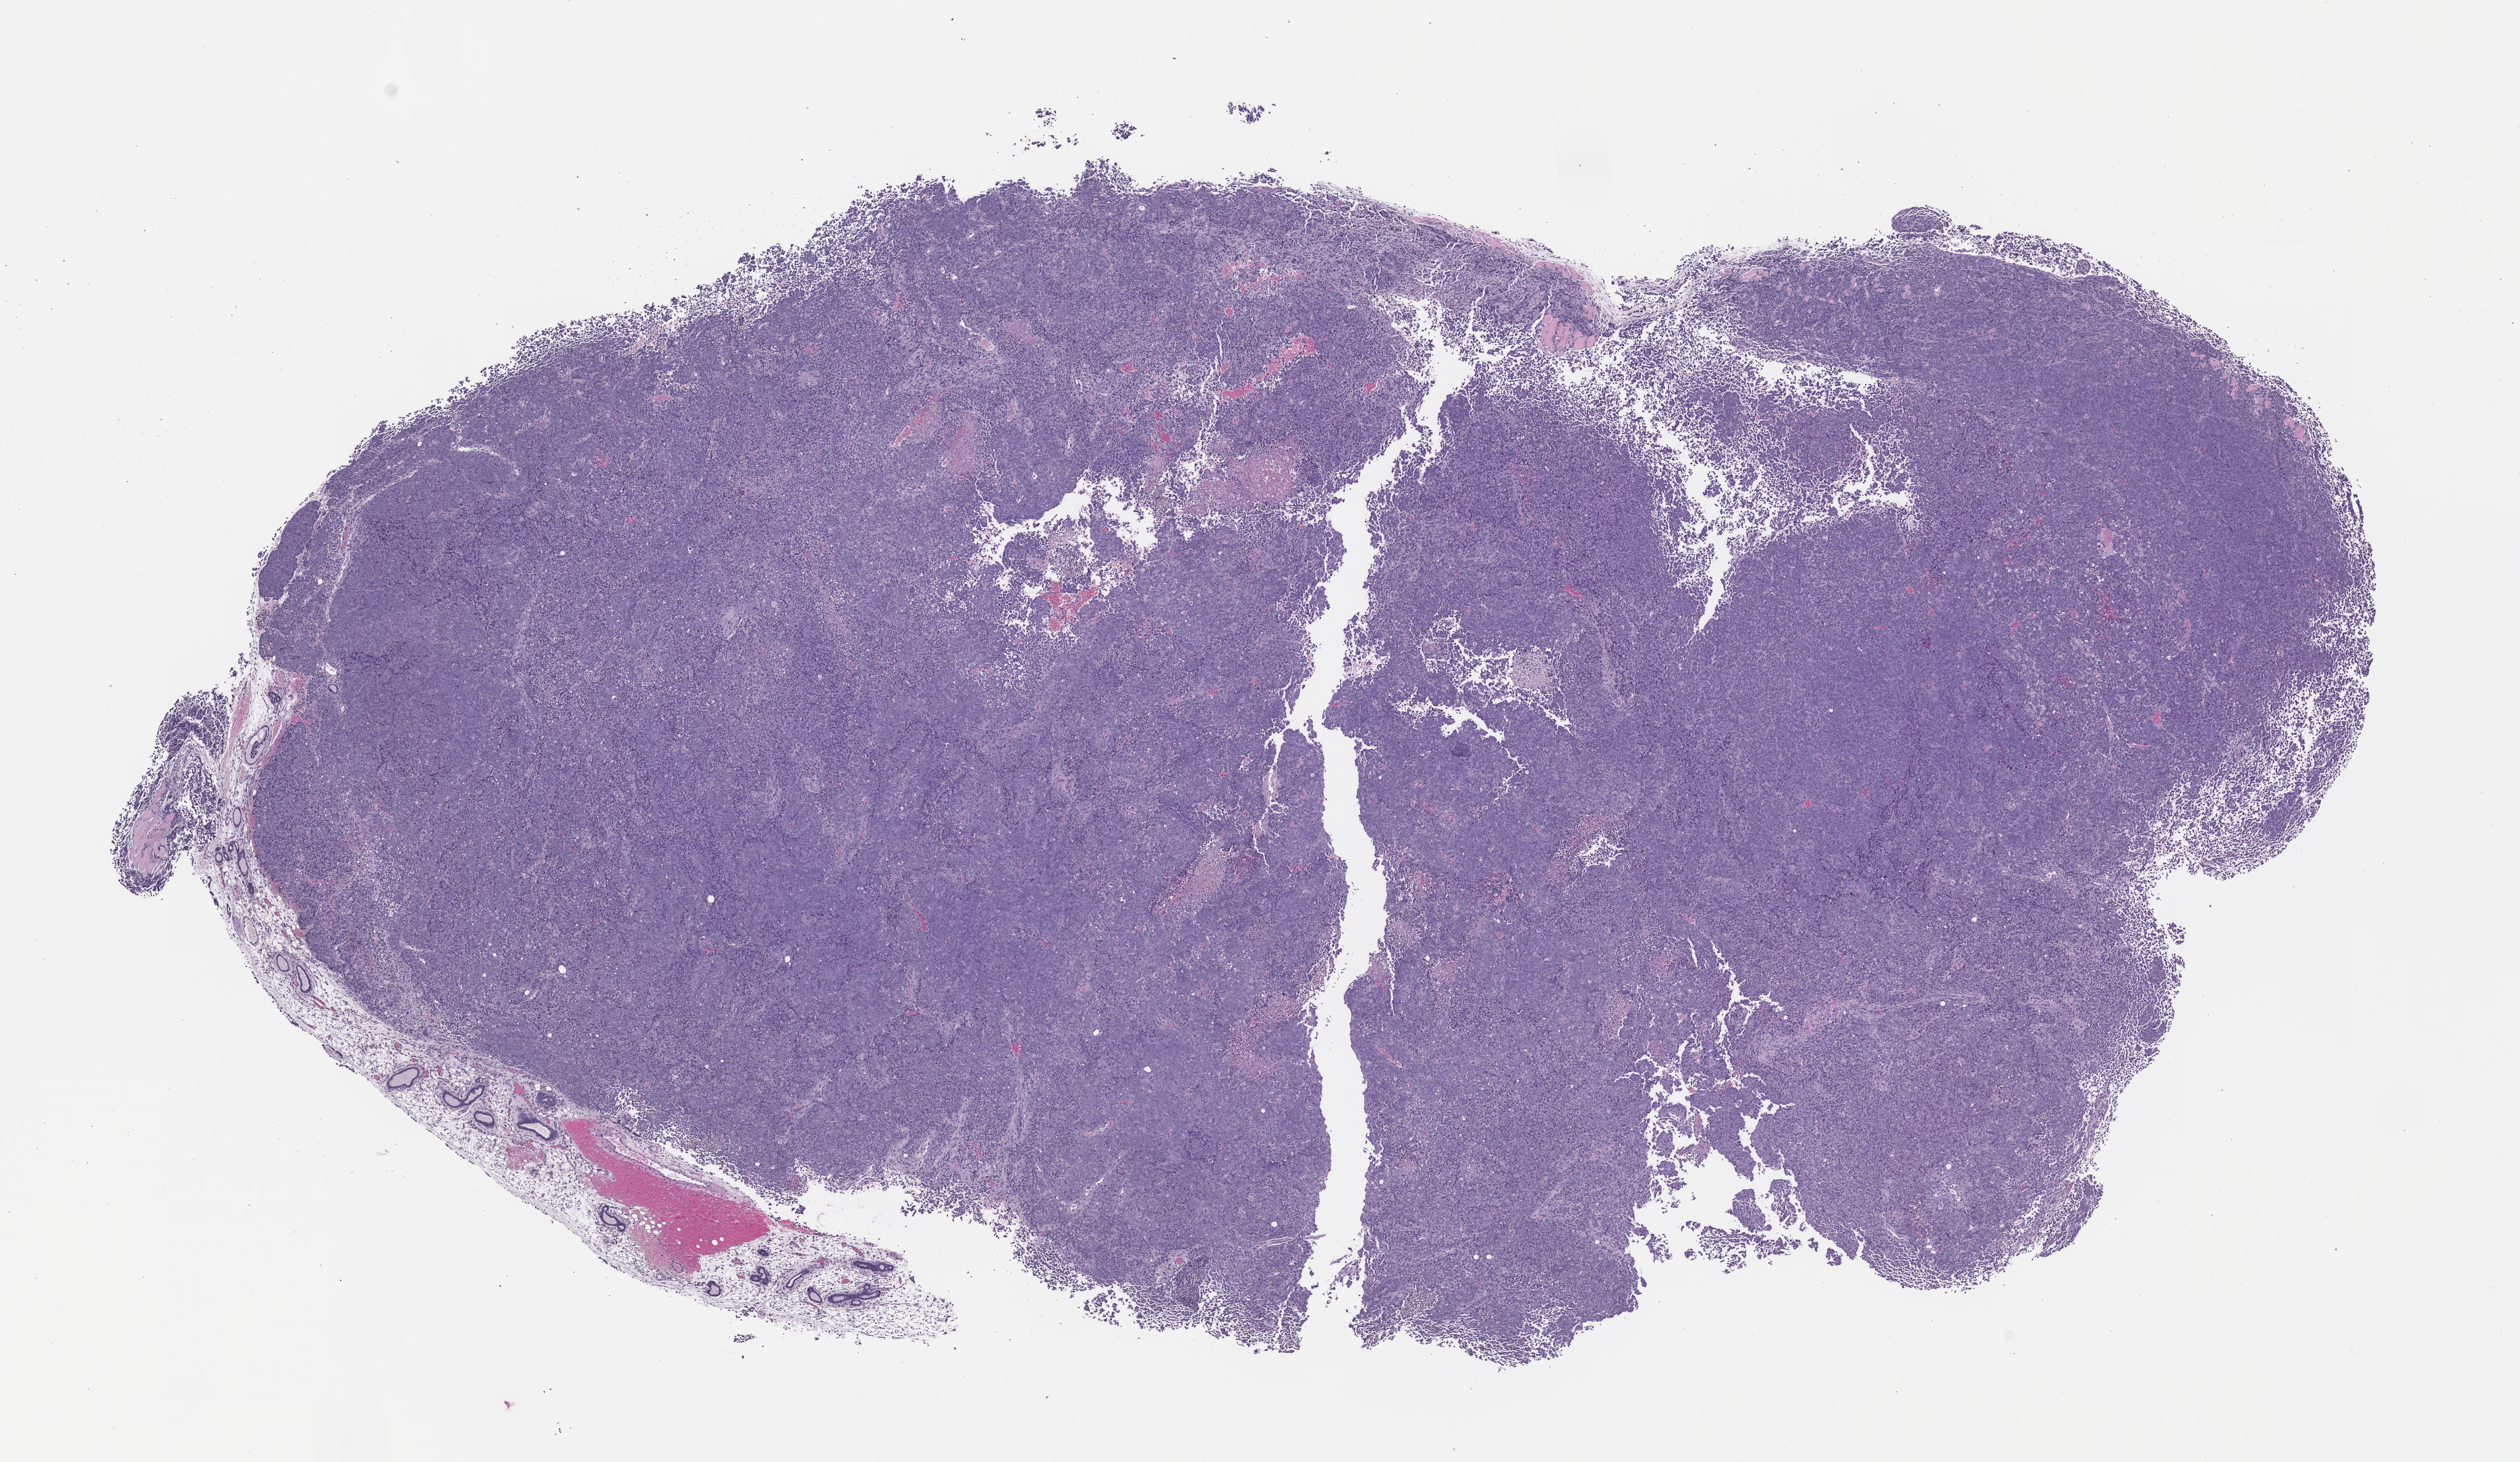
H&E whole-slide image of a patient-derived xenograft (PDX) tumor grown in a mouse, passage 1, whole scanned area (about 15.0 x 8.7 mm) shown as a low-resolution overview, formalin-fixed, paraffin-embedded (FFPE) tissue, originating tumor site category: uterus.
Originating patient diagnosis: Carcinosarcoma.